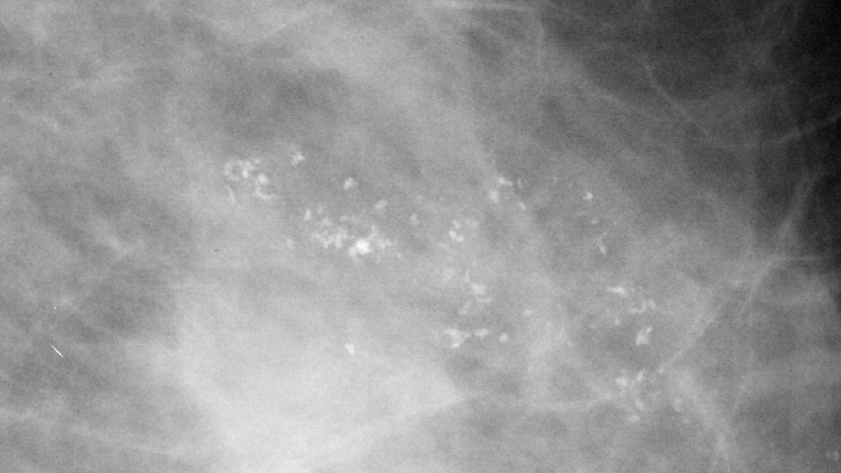
Cropped region of a digitized screen-film mammogram centred on a radiologist-marked abnormality, left breast, MLO view, BI-RADS breast density category 3 (scale 1–4).
- Calcifications, morphology pleomorphic, distribution clustered / segmental; BI-RADS assessment category 4; subtlety rating 4 on a 1 (subtle) to 5 (obvious) scale; pathology result (as recorded, not read from the image): benign.